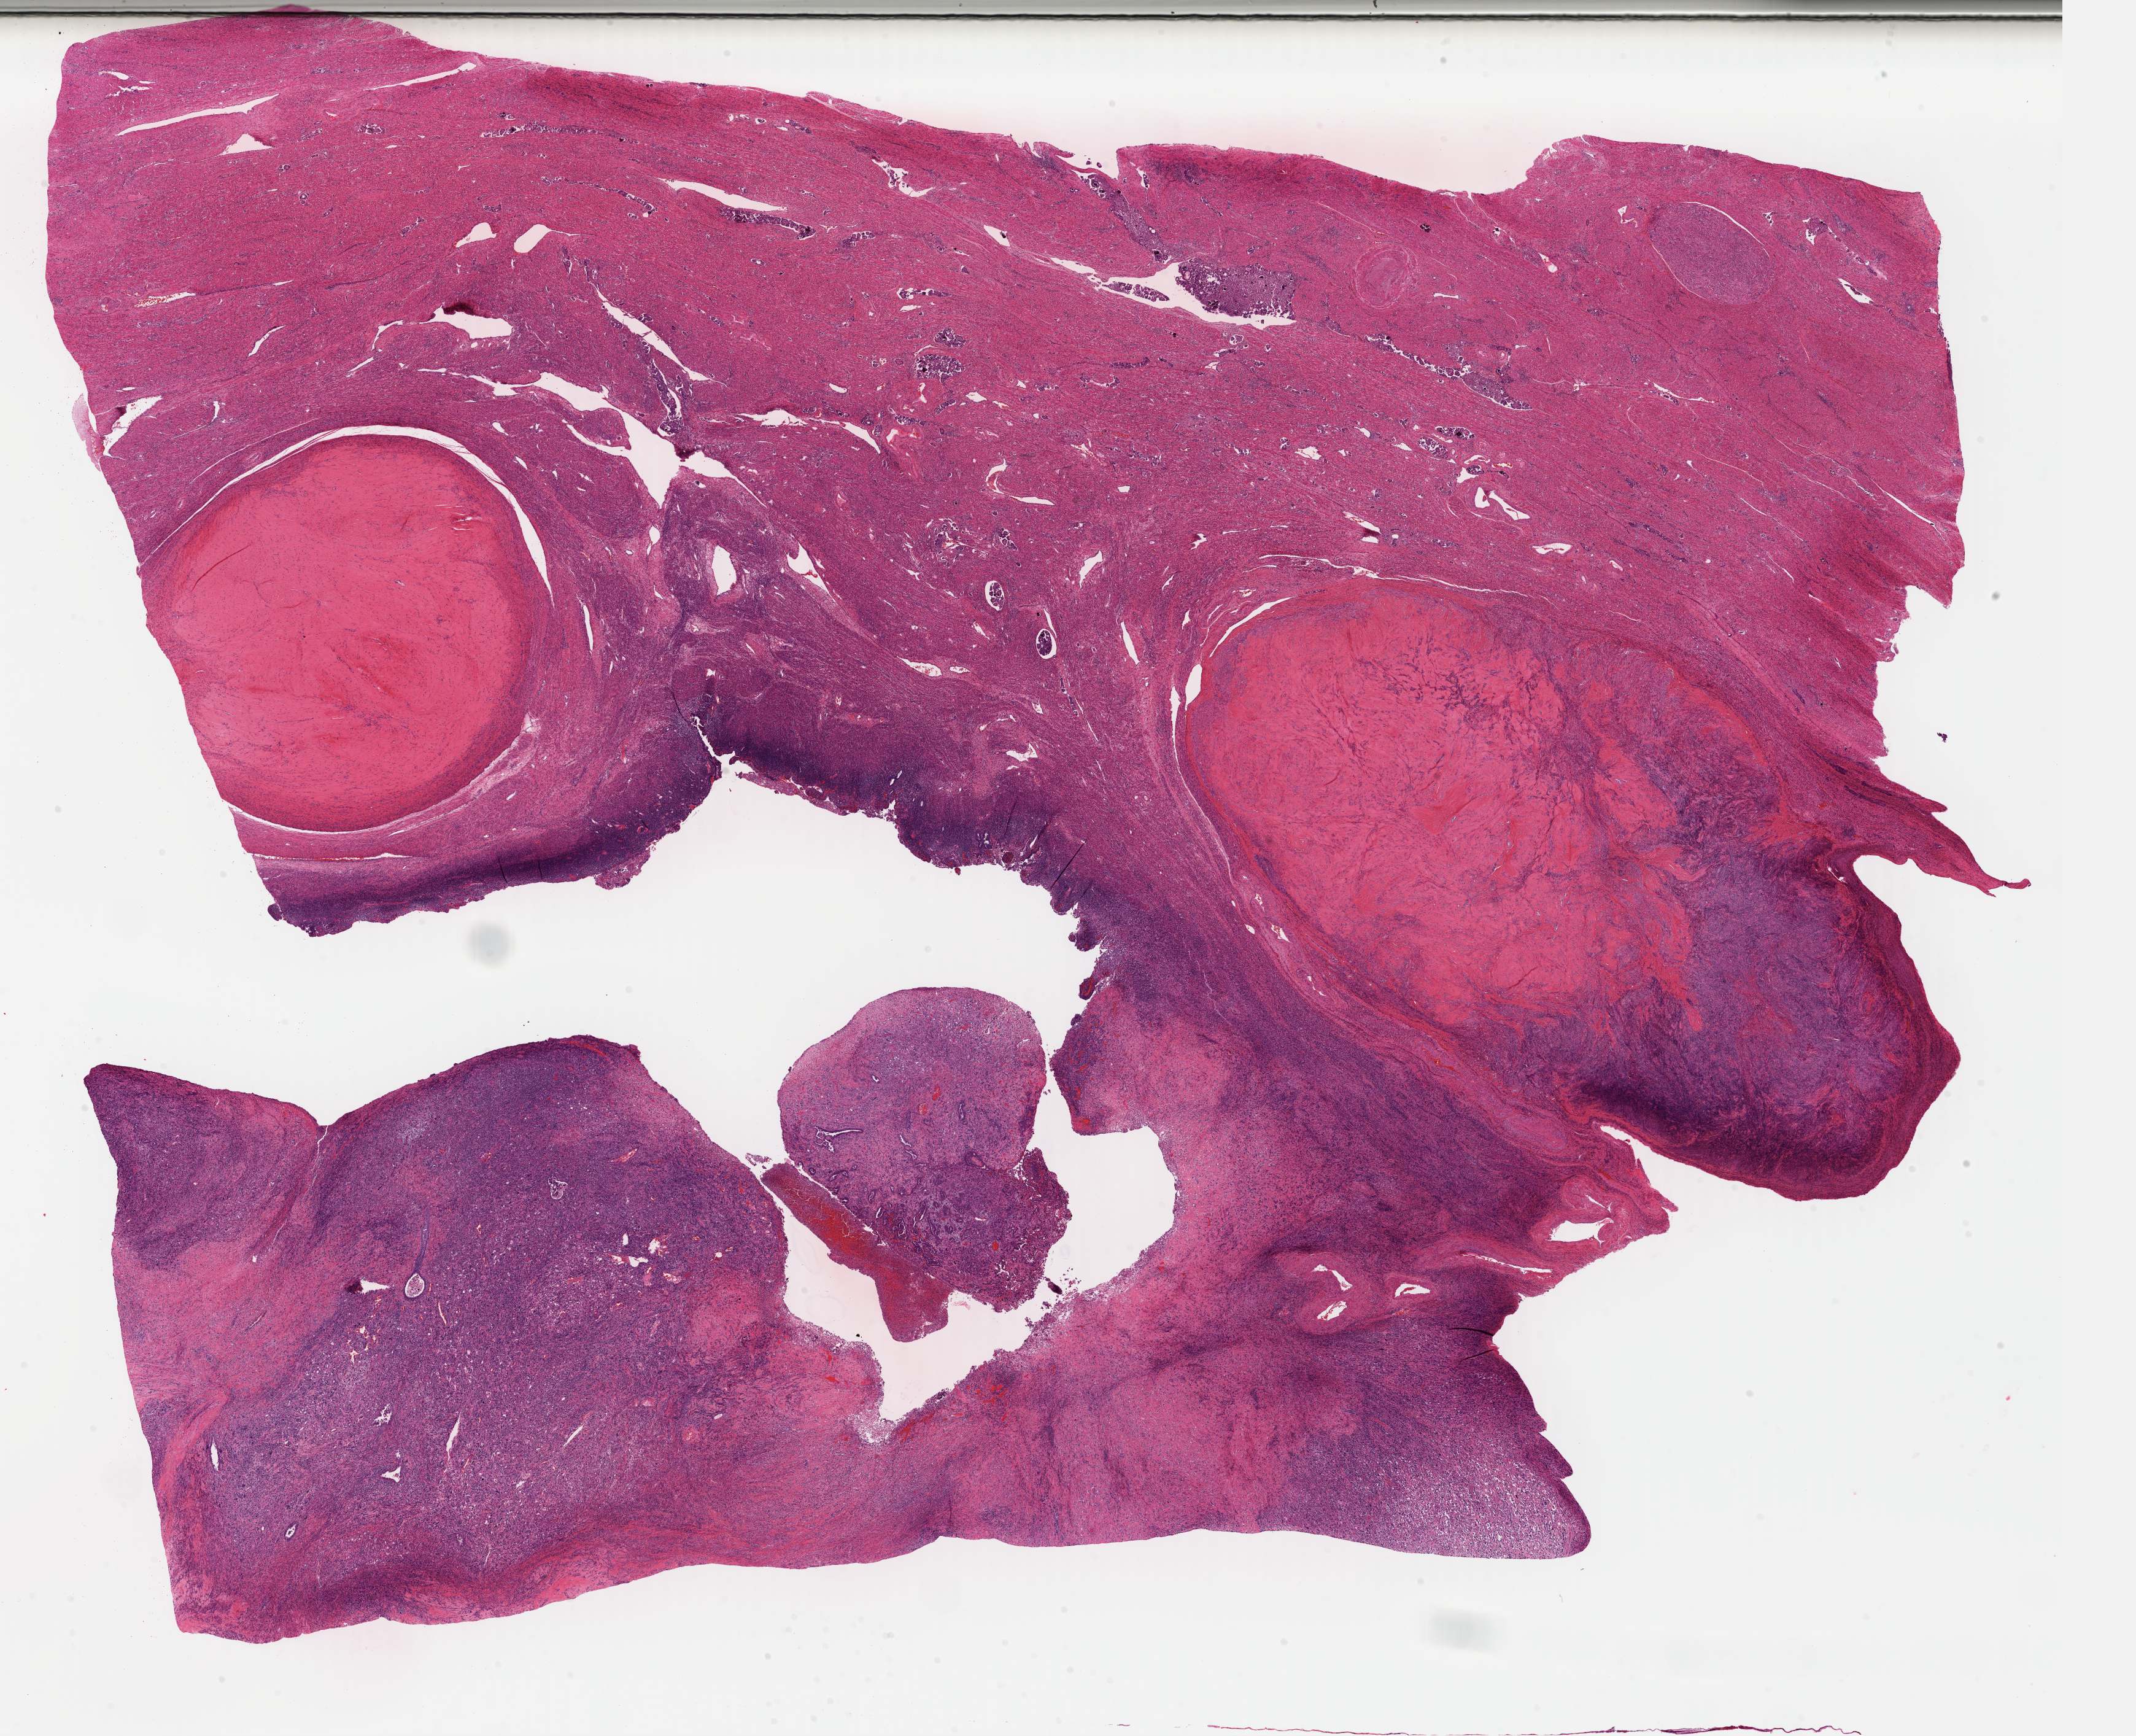
Whole-slide histology image, Hematoxylin and eosin (H&E) stained, whole scanned area (about 27.4 x 22.2 mm, from a 40x scan) shown as a low-resolution overview, formalin-fixed paraffin-embedded (FFPE) diagnostic section, primary tumour sample from the uterus. Female, age 67 years at initial diagnosis.
FIGO stage: IIIC. Diagnosis: Mullerian mixed tumor (endometrium).